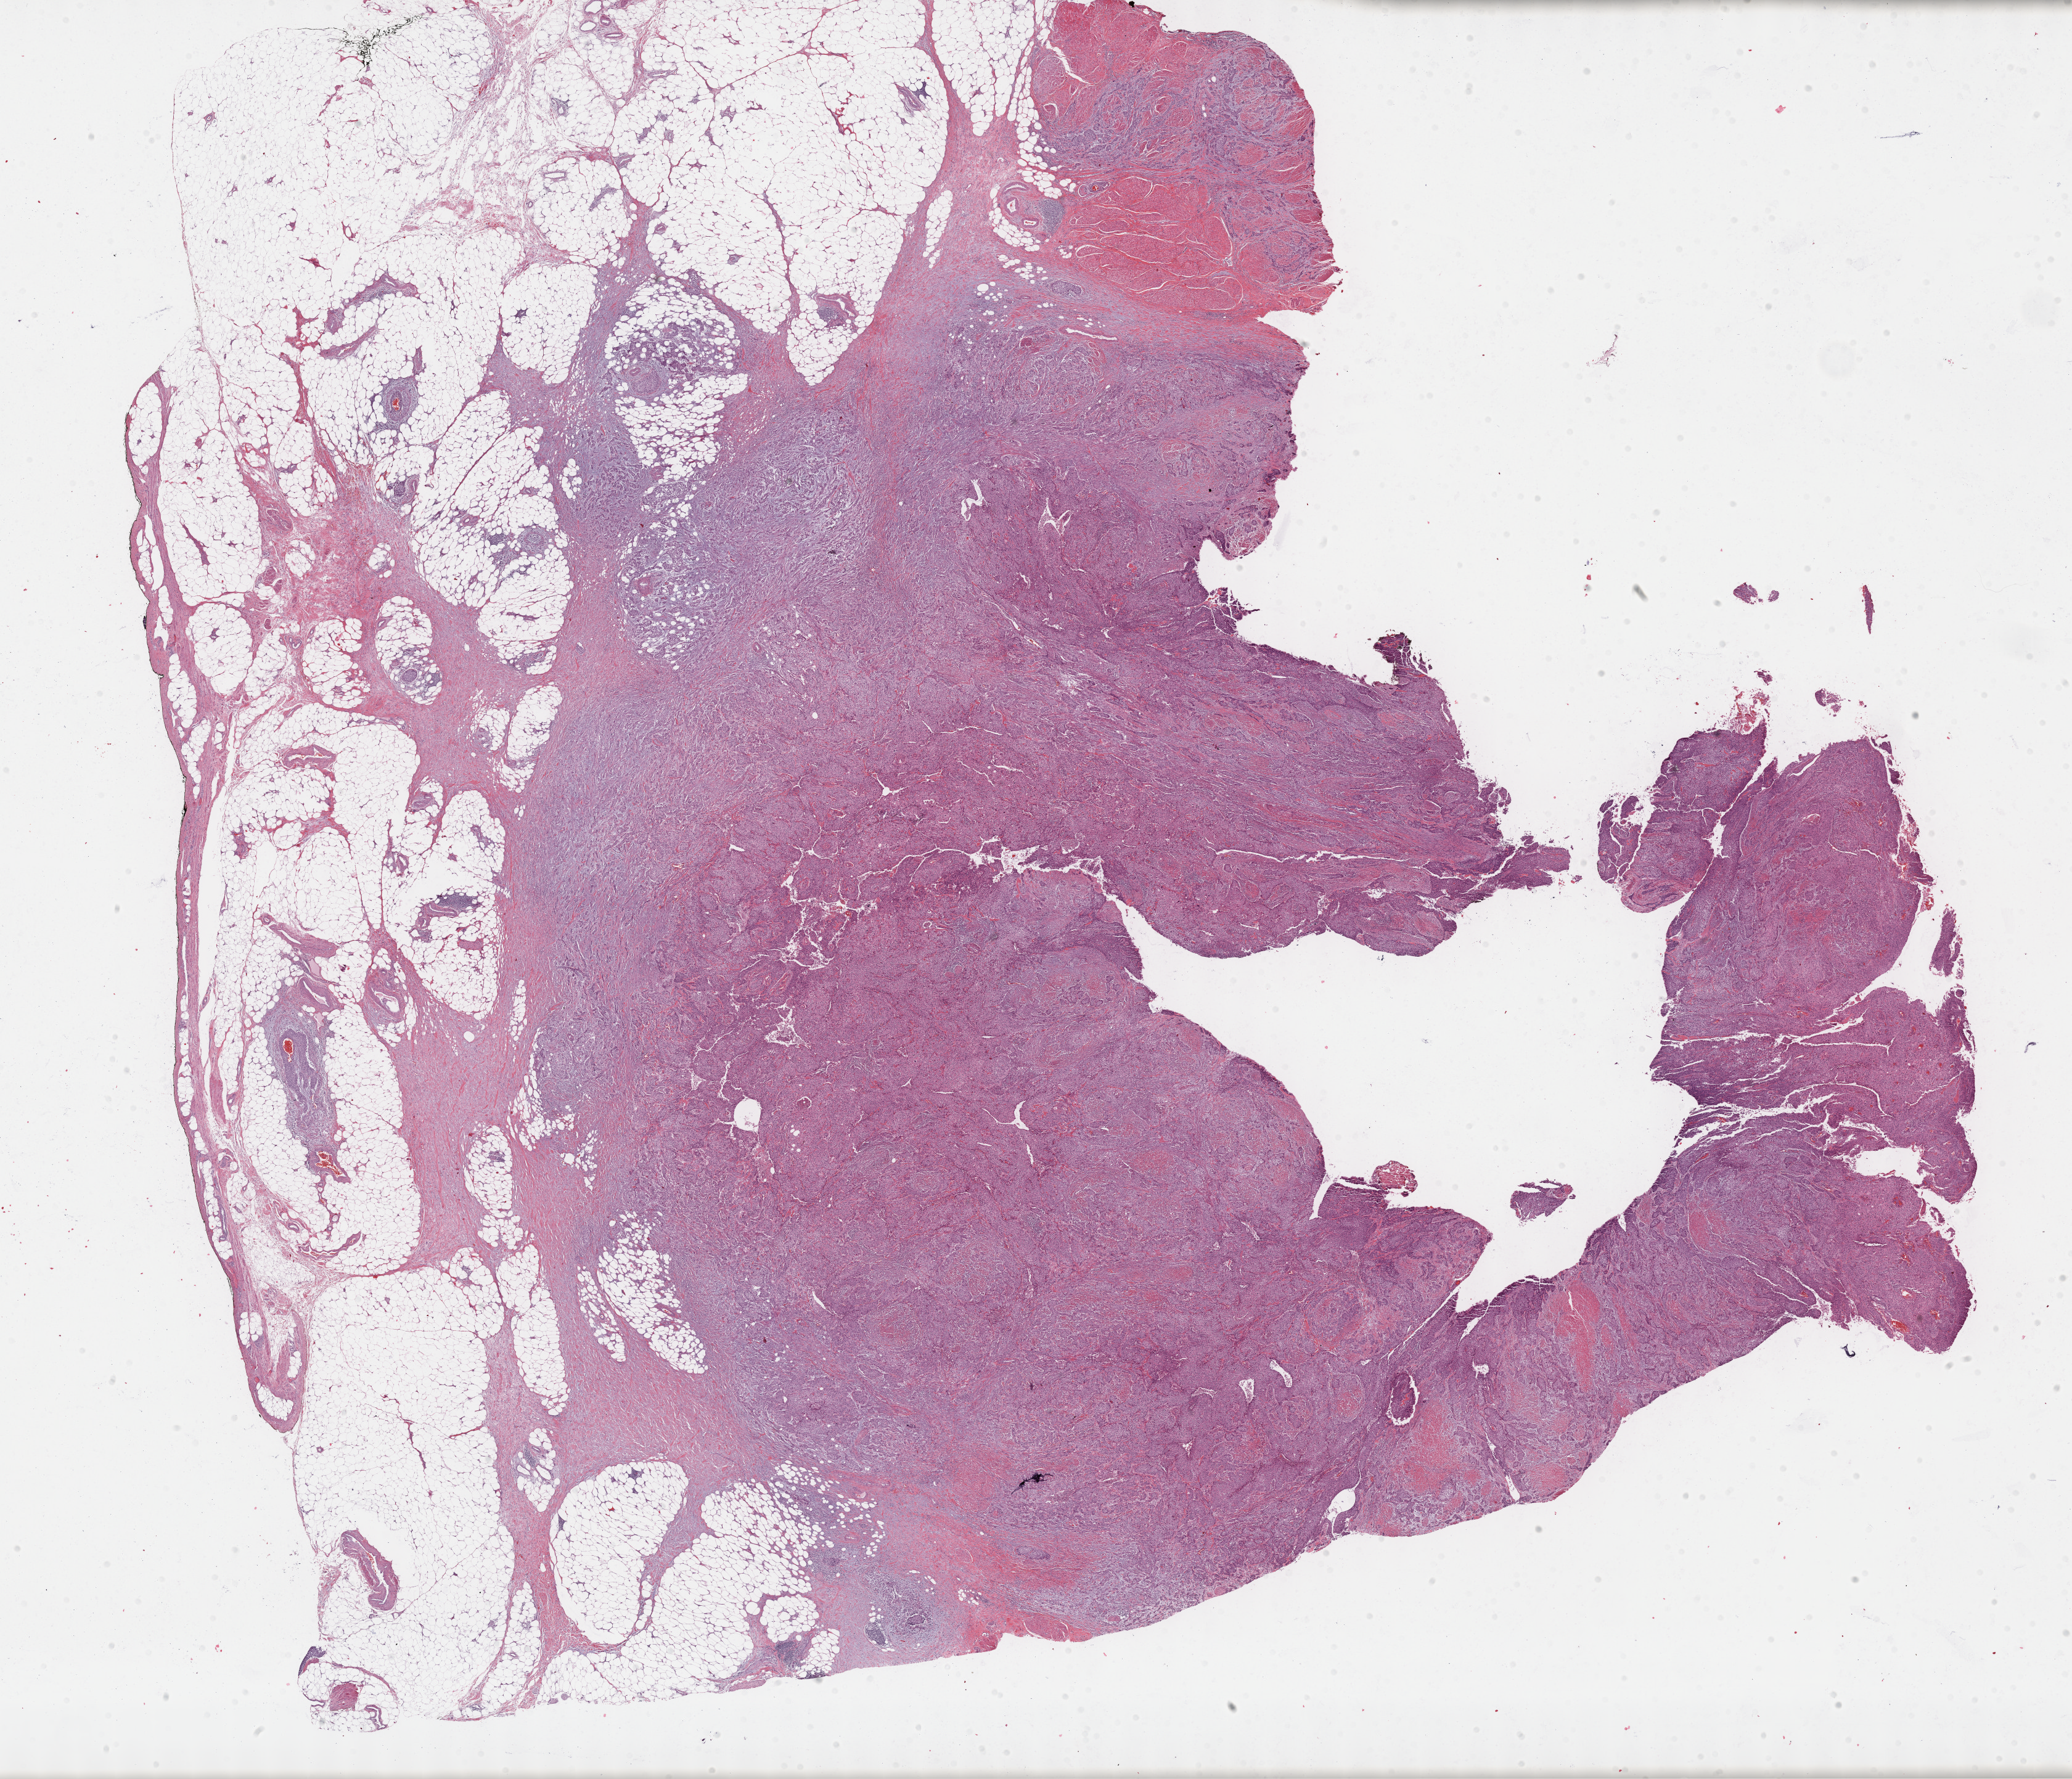
Whole-slide histology image, H&E-stained, a low-resolution overview of the entire scanned area, about 27.2 x 23.3 mm, formalin-fixed paraffin-embedded (FFPE) diagnostic section, primary tumour sample from the bladder. Male, age 65 years at initial diagnosis. Histologic grade: high grade.
Diagnosis: Transitional cell carcinoma. AJCC pathologic stage: IV. TNM: T3b N1 MX. Lymph nodes positive (case pathology): 3 of 108 examined.